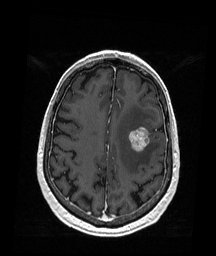
Brain MRI from a brain-tumour surgery series, one axial slice; slice 61 of 176 in the series (ordered by position); T1-weighted post-contrast; 1 mm slice thickness; 216 × 256 image matrix, field of view 211 × 250 mm. From the clinical record (not read from this slice): histopathology: Metastatic Melanoma.
Structures marked on this image (expert manual segmentation):
- tumour: bounding box (x1, y1, x2, y2) in pixels: (129, 127, 151, 151)